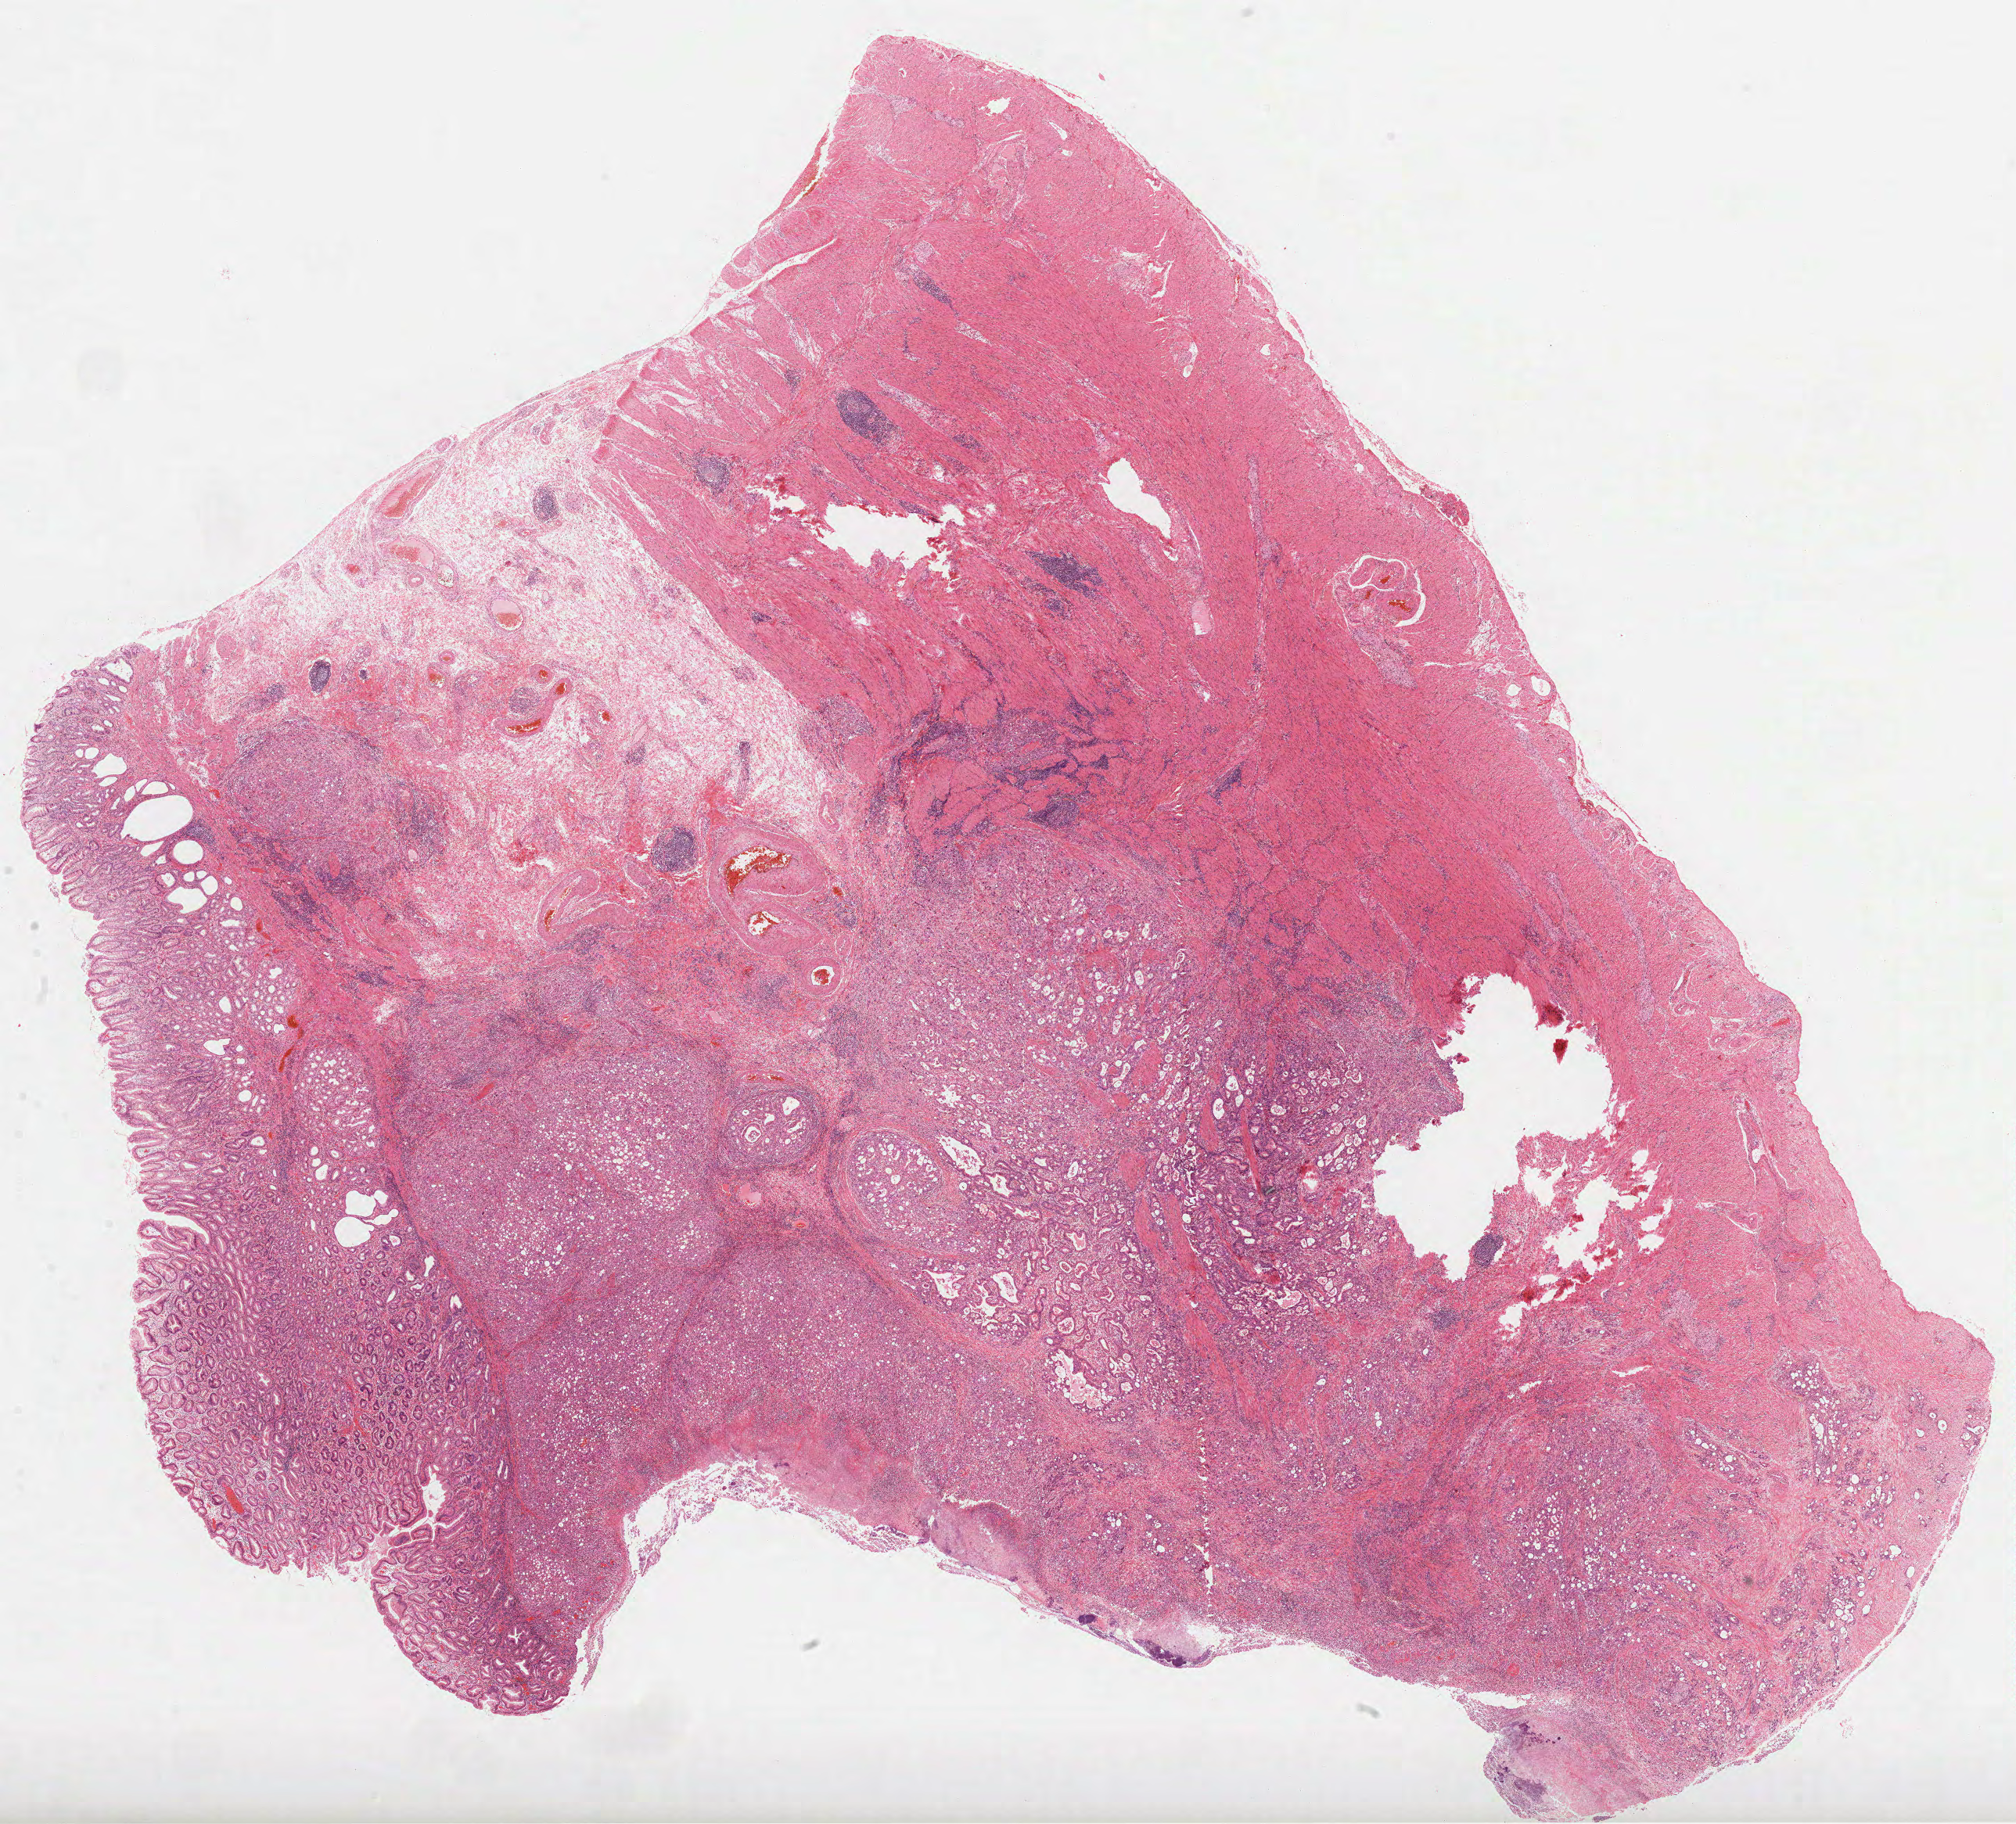
Digitized H&E-stained tissue section (whole slide), shown as a low-resolution overview of the whole scanned area (about 20.8 x 18.8 mm, acquisition: 40x scan); formalin-fixed paraffin-embedded (FFPE) diagnostic section; sample: primary tumour, stomach. Male, age 75 years at initial diagnosis. Histologic grade: G3 (poorly differentiated).
AJCC pathologic stage: IIIB. Histologic diagnosis: Tubular adenocarcinoma (gastric antrum). TNM: T4a N2 M0. Lymph nodes positive (case pathology): 3 of 5 examined.